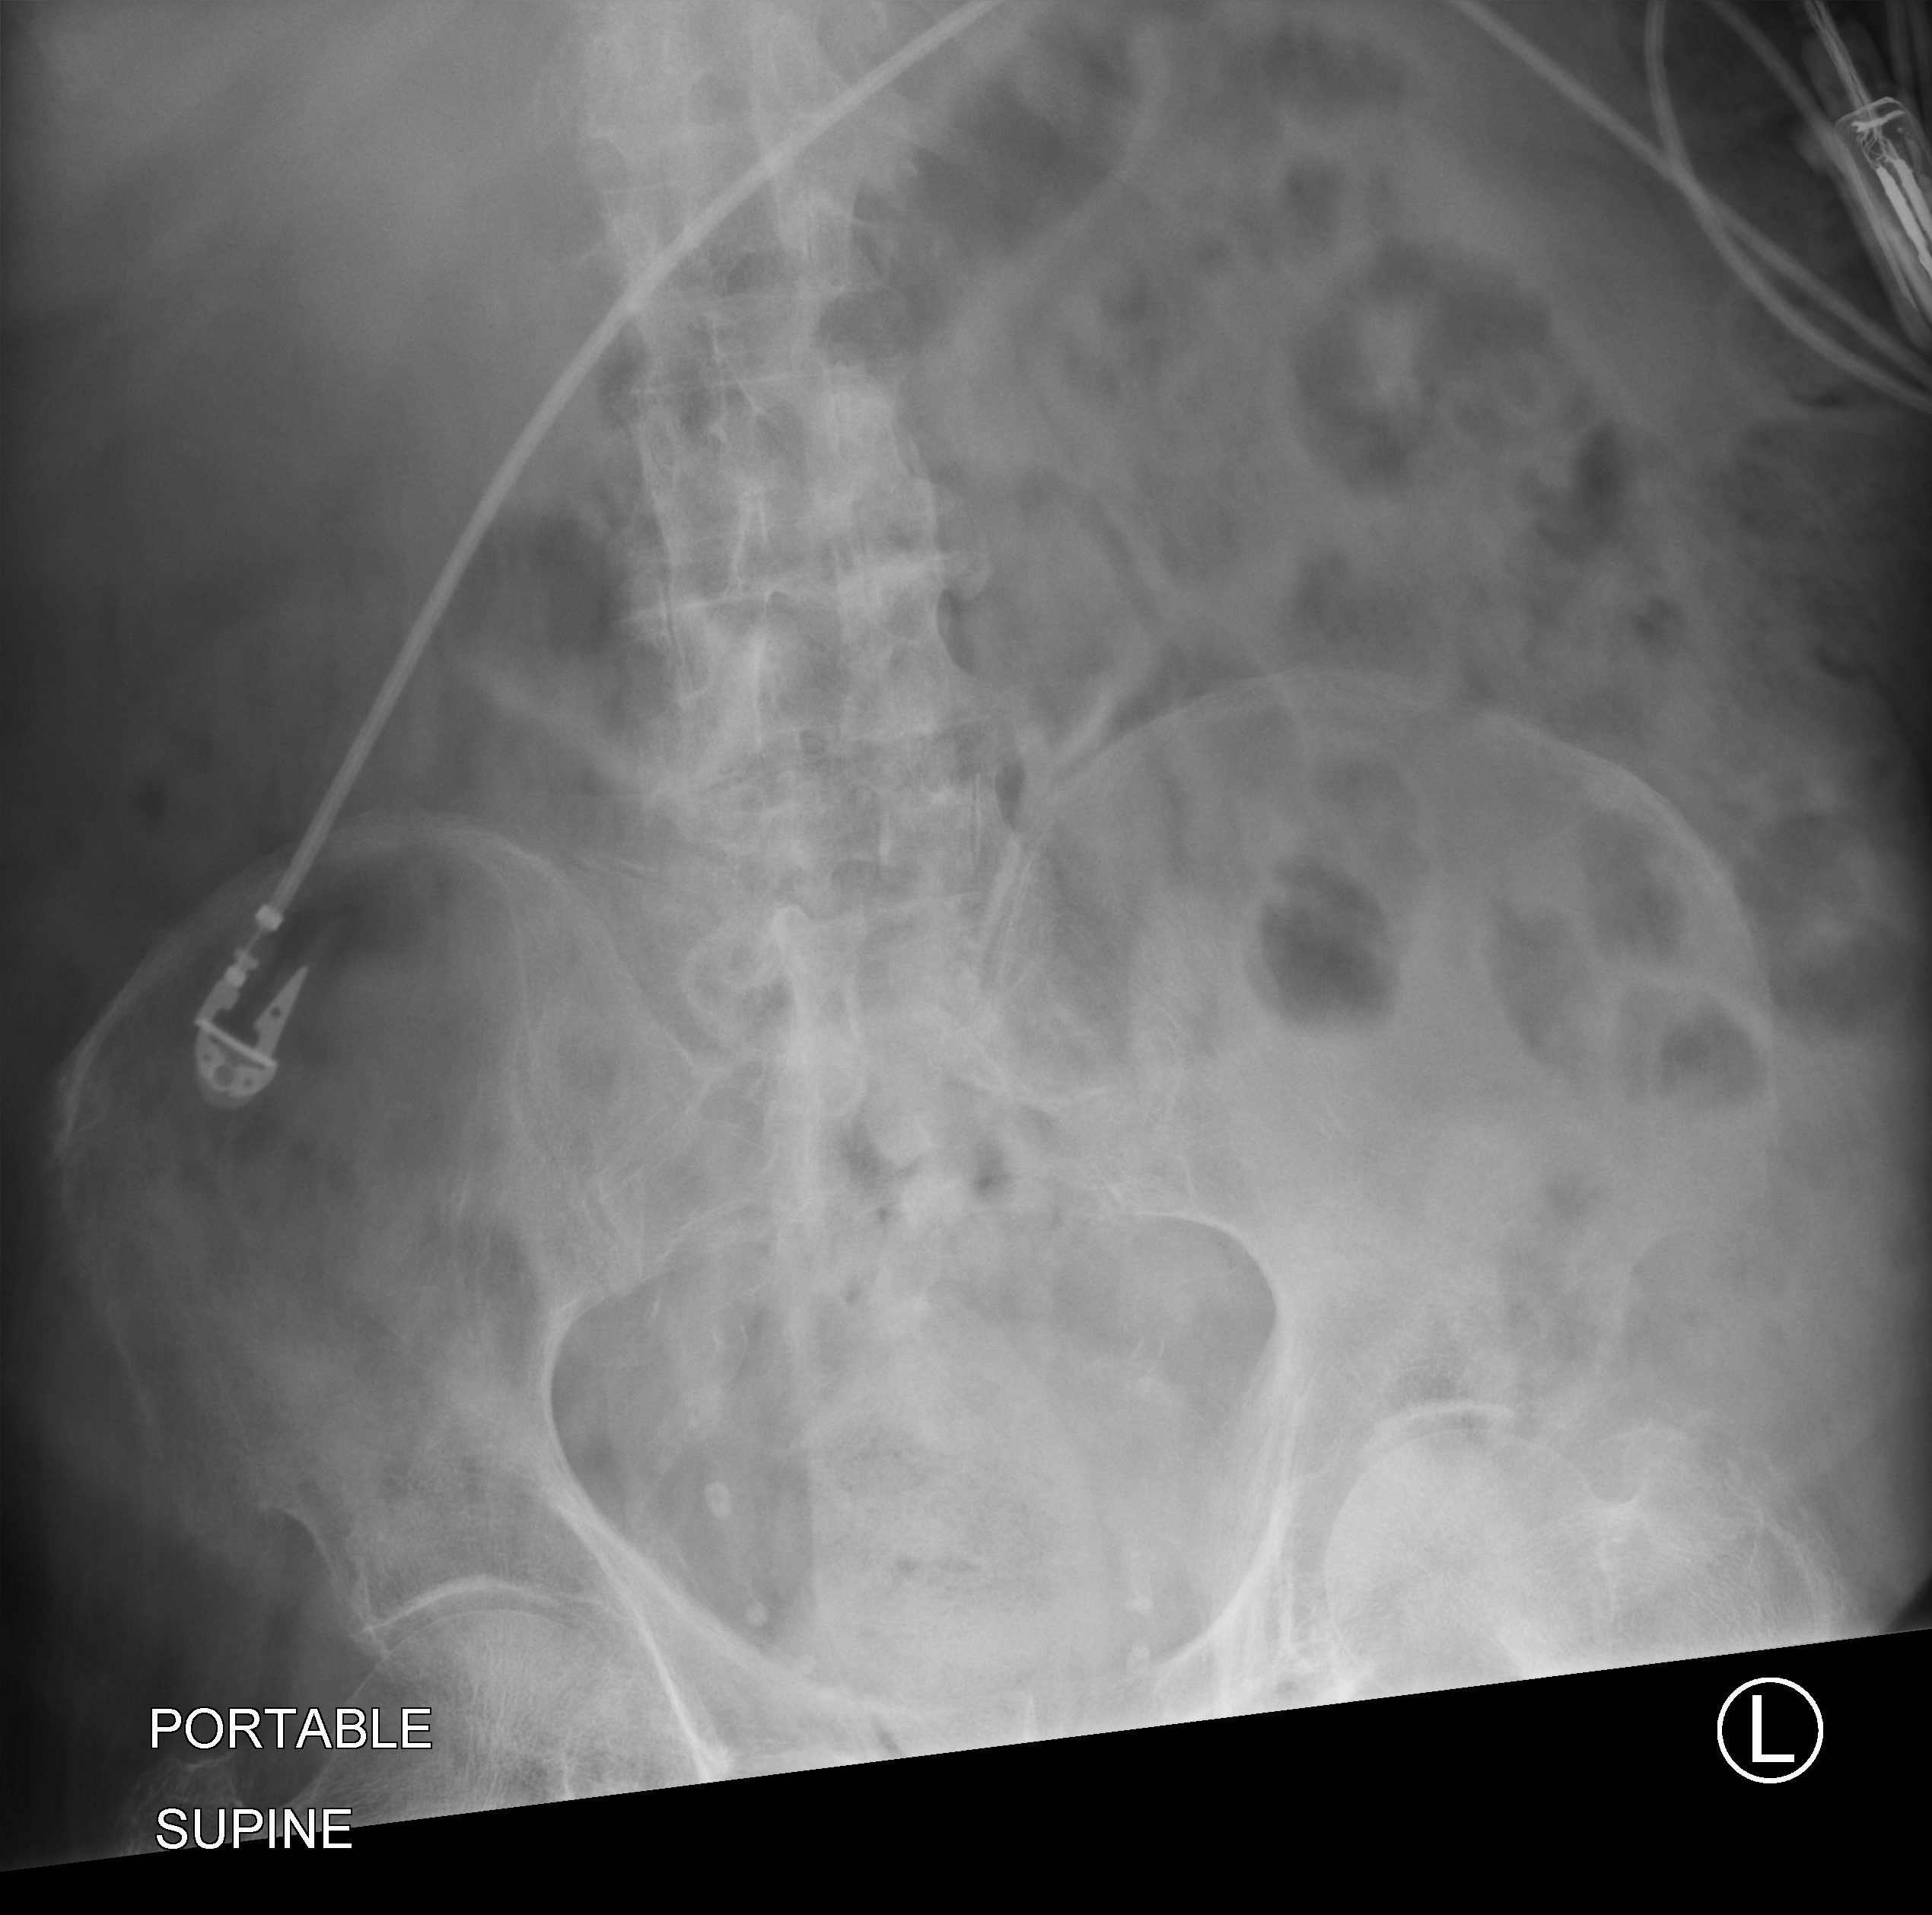
Abdomen X-ray (portable). Male patient hospitalised with COVID-19, age 75–90 years.
Admission-level facts for this patient (not findings on this image; timing relative to this image not recorded):
- hypertension (admission record): yes